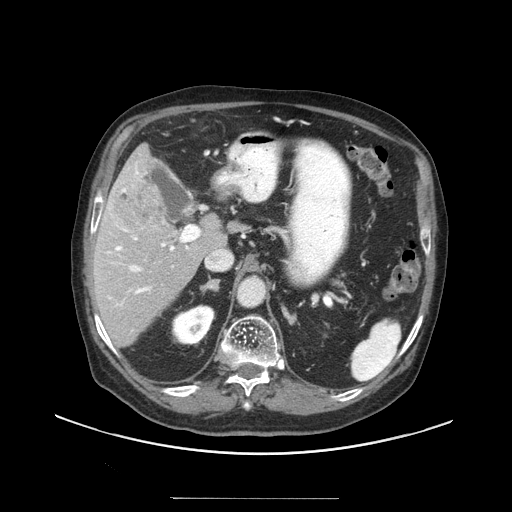
Contrast-enhanced abdominal CT (liver protocol), one axial slice; slice 60 of 97 in the series (ordered by position); 140 kVp; soft-tissue window (W 400 / L 40 HU); 2.5 mm slice thickness; 512 × 512 image matrix, field of view 450 × 450 mm. From the clinical record (not read from this slice): diagnosis: hepatocellular carcinoma (patient treated with transarterial chemoembolisation; whether this scan precedes or follows treatment is not stated here); TNM stage (as recorded): Stage-IIIC.
Outlined on this slice (semi-automatically segmented with operator editing):
- liver parenchyma outside the tumour (the mass and vessels are separate outlines, so this box may not span the whole liver): box from (x=92, y=144) to (x=226, y=346) px
- mass: (x=110, y=180)–(x=166, y=235)
- liver vessels: (x=107, y=167)–(x=188, y=298)